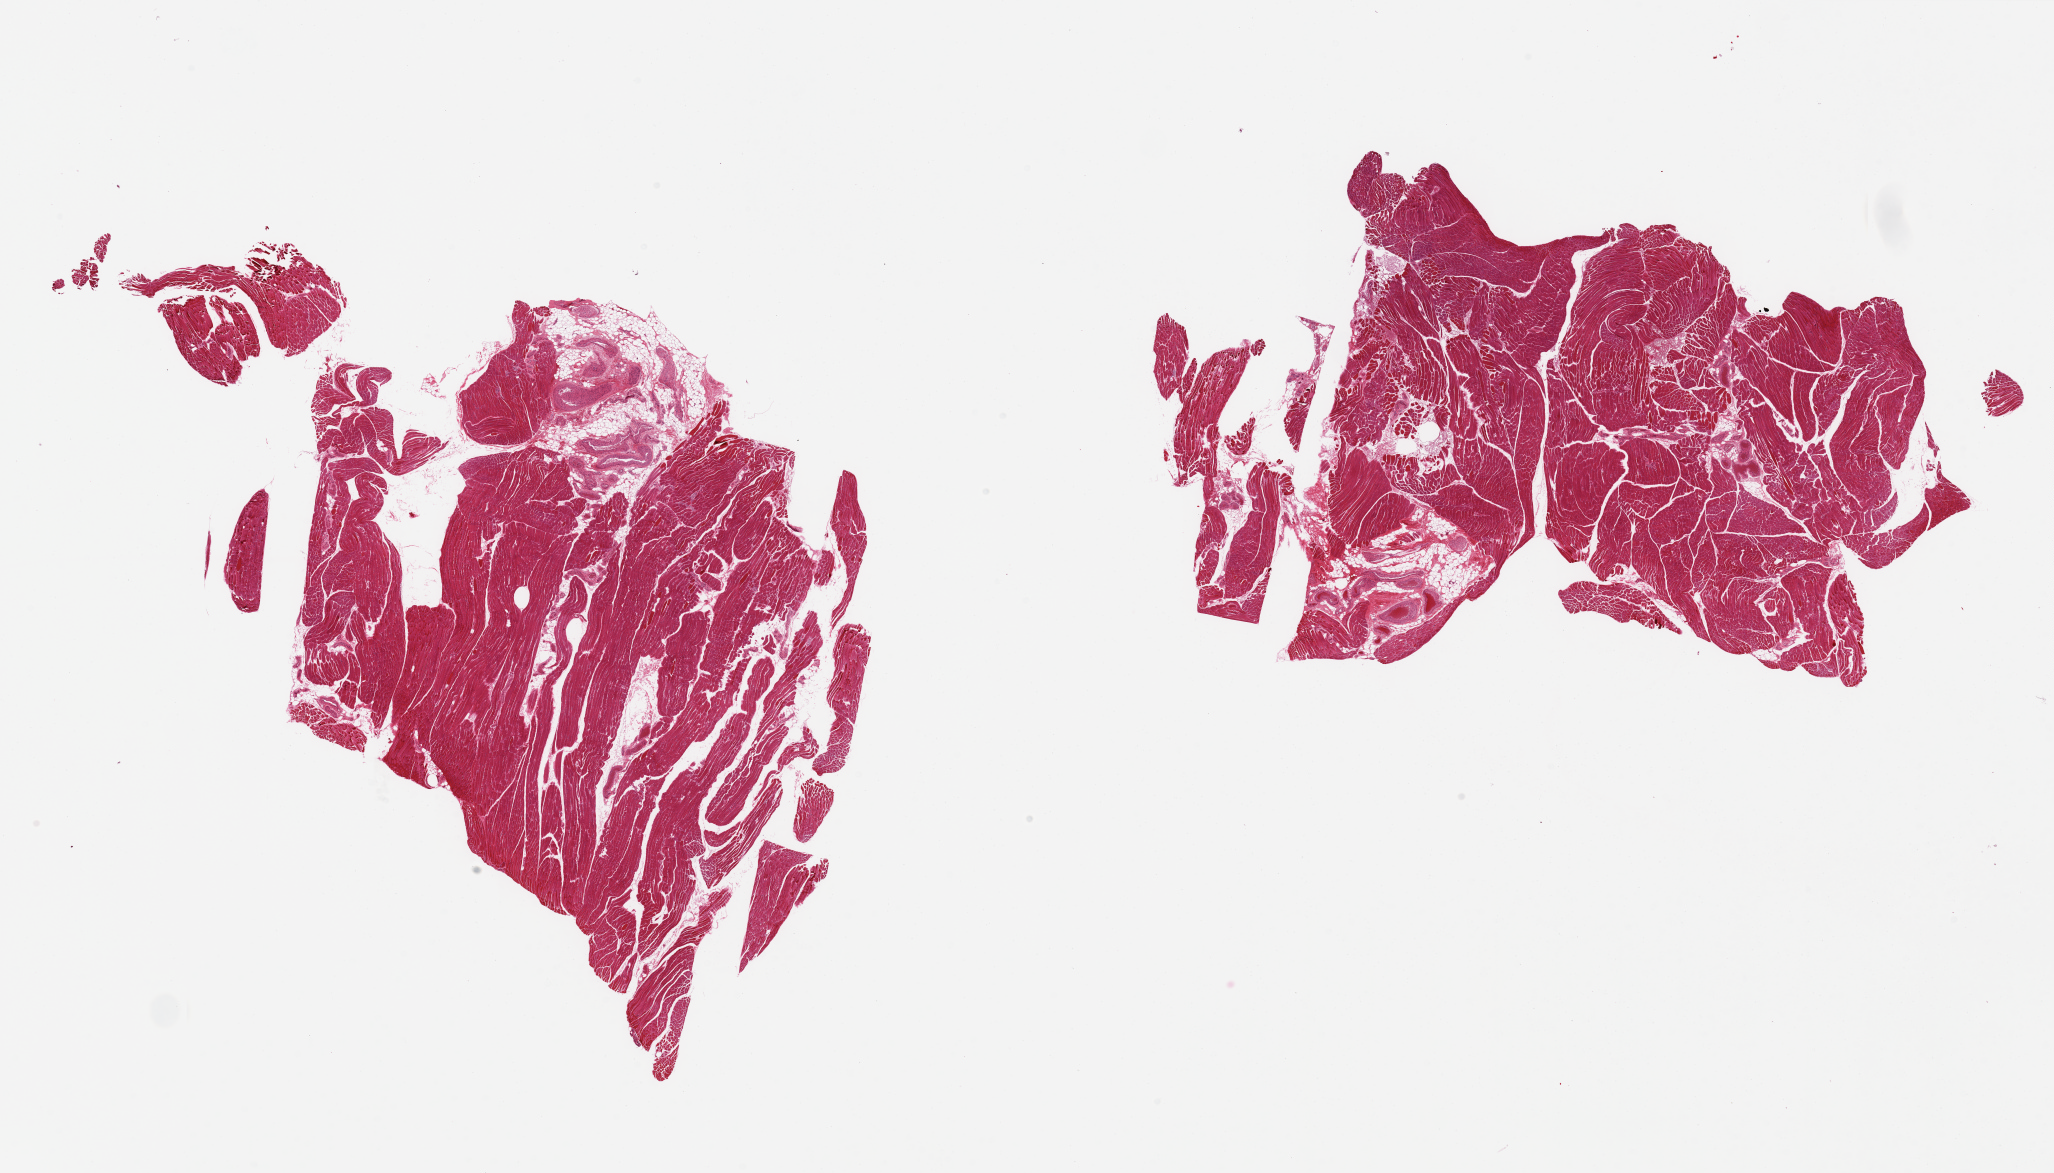
Digitized haematoxylin and eosin-stained section — a low-resolution overview of the entire scanned area, about 32.5 x 18.6 mm; PAXgene-fixed, paraffin-embedded tissue; section of skeletal muscle (target tissue); tissue donor sample.
Review note (as recorded): 2 pieces; ~10% interstitial/adherent fibroadipose tissue.